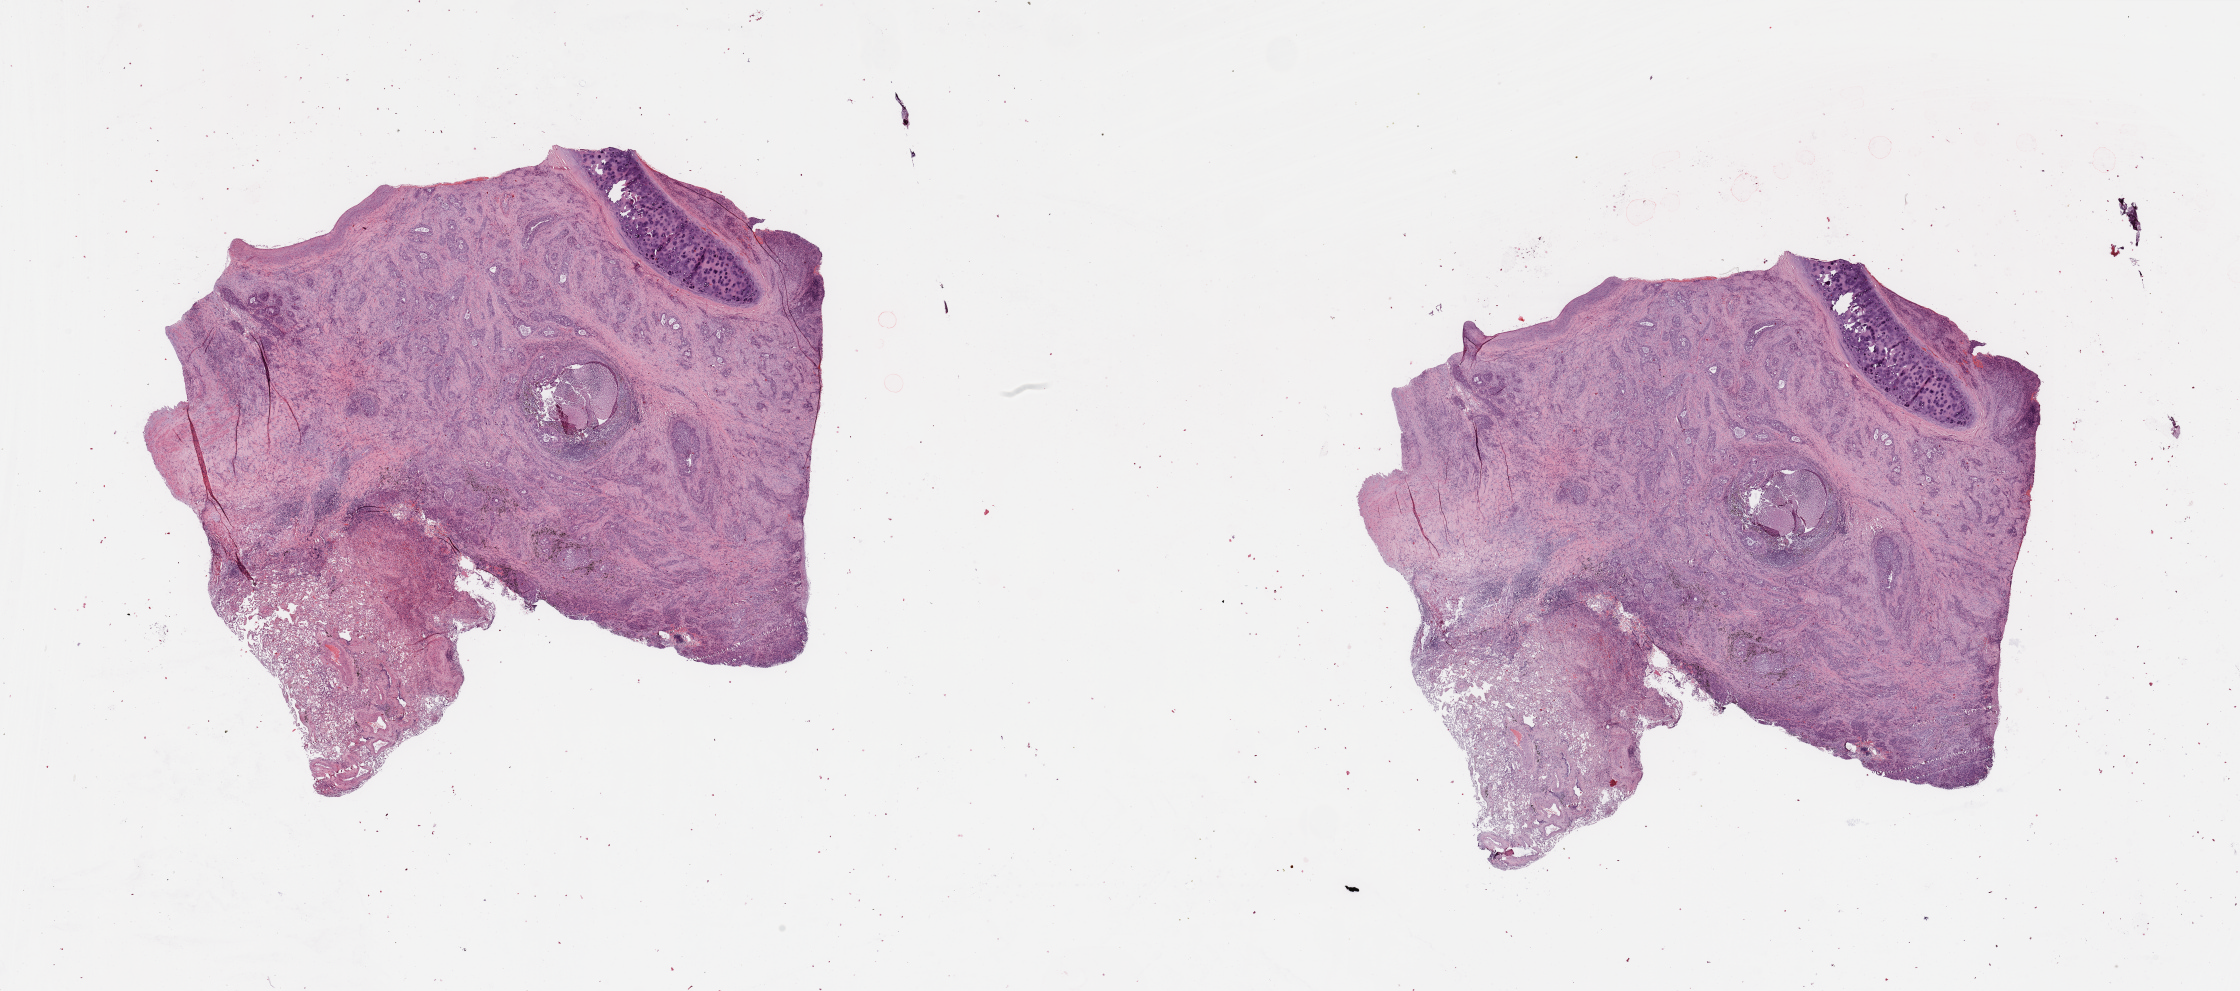
Whole-slide histology image, H&E — a low-resolution overview of the entire scanned area, about 35.4 x 15.7 mm, tumour tissue sample, lung. Male, 72 y/o.
Histologic diagnosis: Squamous cell carcinoma, NOS.